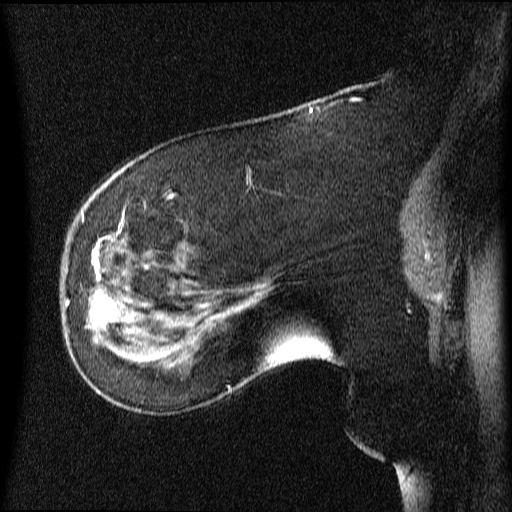
Breast MRI (dynamic contrast-enhanced), one sagittal slice; slice 24 of 64 in the series (ordered by position); dynamic contrast-enhanced series, image 2 of 4 at this slice position (ordered by acquisition); 1.5 T; TE 4.2 ms, TR 9 ms; 512 × 512 image matrix, field of view 200 × 200 mm. Patient: female, 63 years.
Annotated regions visible in this slice (semi-automatic segmentation, software-assisted and operator-edited):
- analysis volume of interest (the breast-tissue region the enhancement analysis was run in; not a lesion): bounding box [x1, y1, x2, y2] px = [66, 272, 131, 353]
- tumour enhancement mask (voxels above the 70 % enhancement threshold inside the analysis volume of interest): [89, 290, 129, 353]